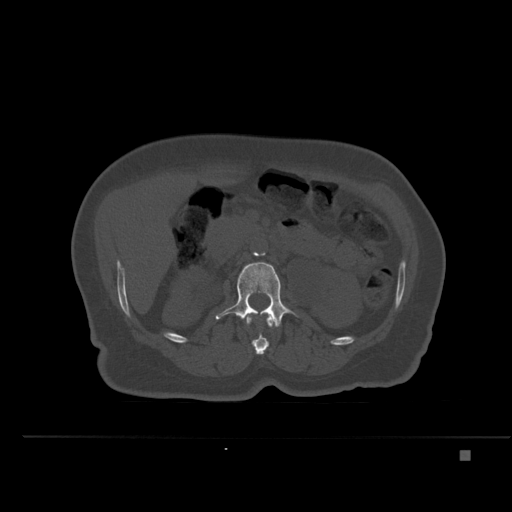
CT including the spine, one axial slice. Position 220 of 477 along the scan axis. Bone window (W 1800 / L 400 HU). 1.5 mm slice thickness. 512 × 512 image matrix, field of view 422 × 422 mm. Female patient, age 74 years. From the clinical record (not read from this slice): primary cancer: colon.
Structures marked on this image (semi-automatic segmentation, software-assisted and operator-edited):
- L1 vertebra: bounding box <246,313,274,355> (left, top, right, bottom; pixels)
- L2 vertebra: <215,262,293,327>